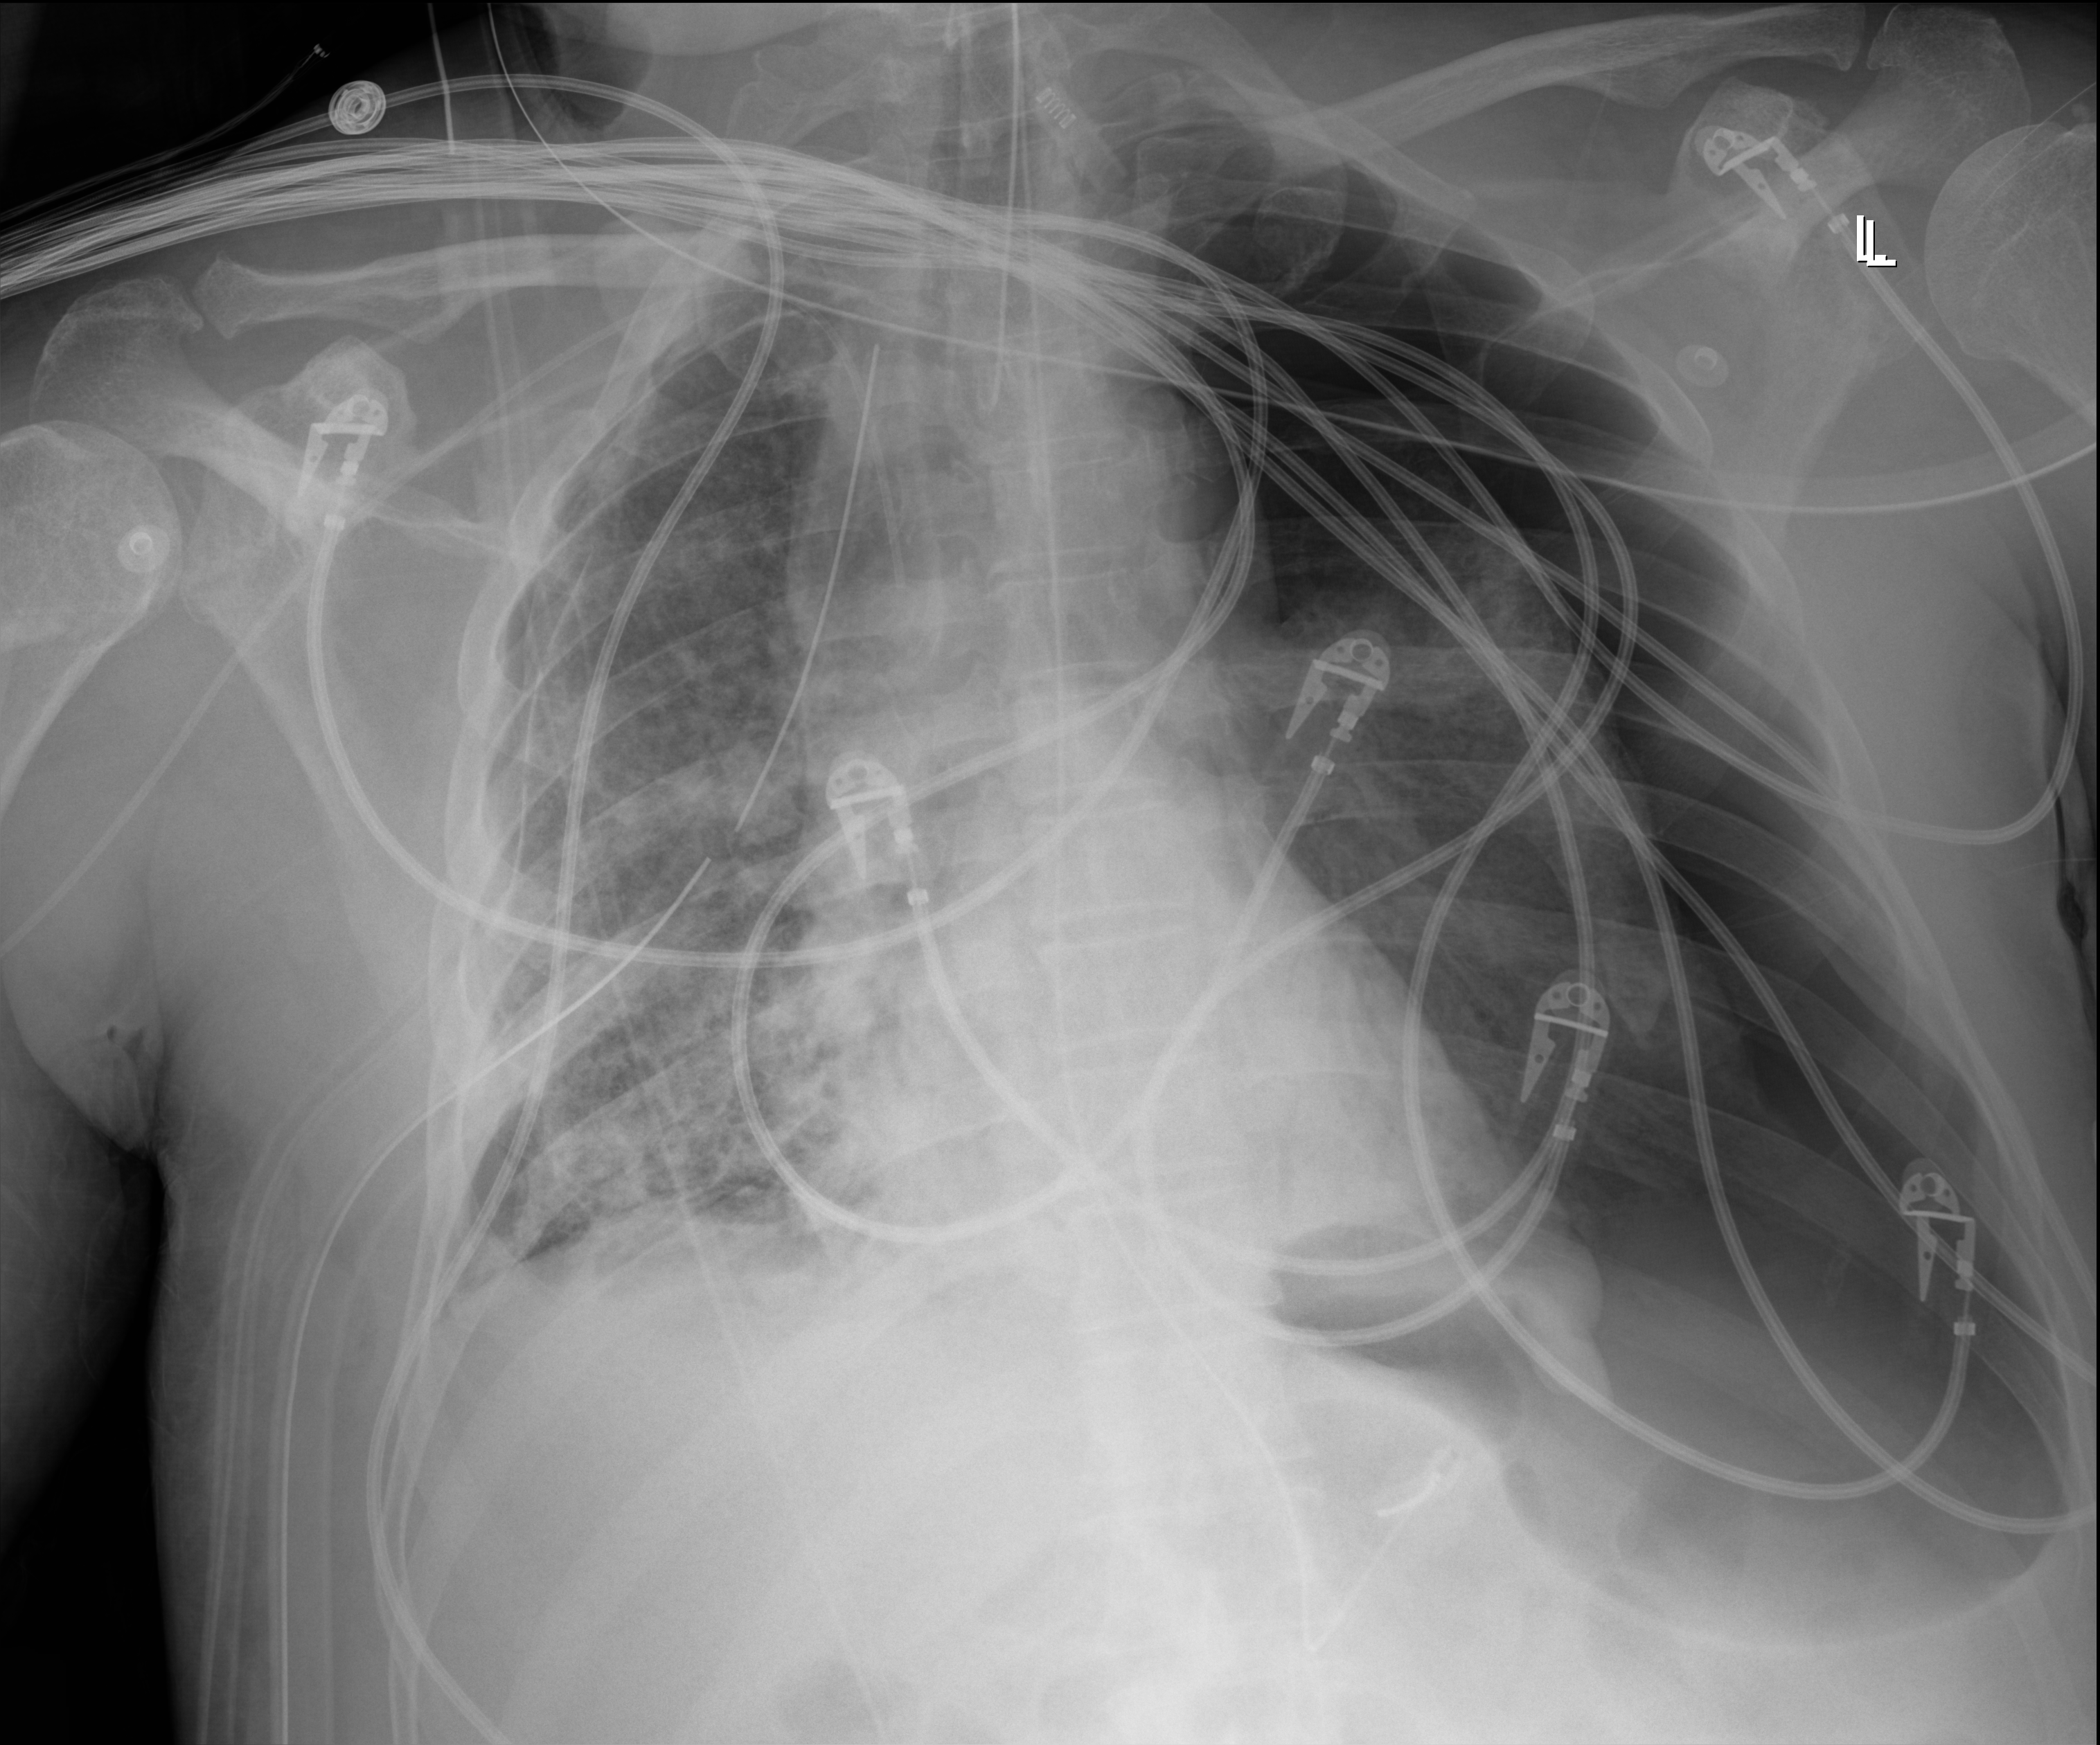
Chest X-ray (portable), anteroposterior (AP) projection. Male patient hospitalised with COVID-19, age 60–74 years.
Admission-level facts for this patient (not findings on this image; timing relative to this image not recorded): mechanically ventilated during this hospital stay: yes; other chronic lung disease (admission record): no; admitted to intensive care during this hospital stay: yes.